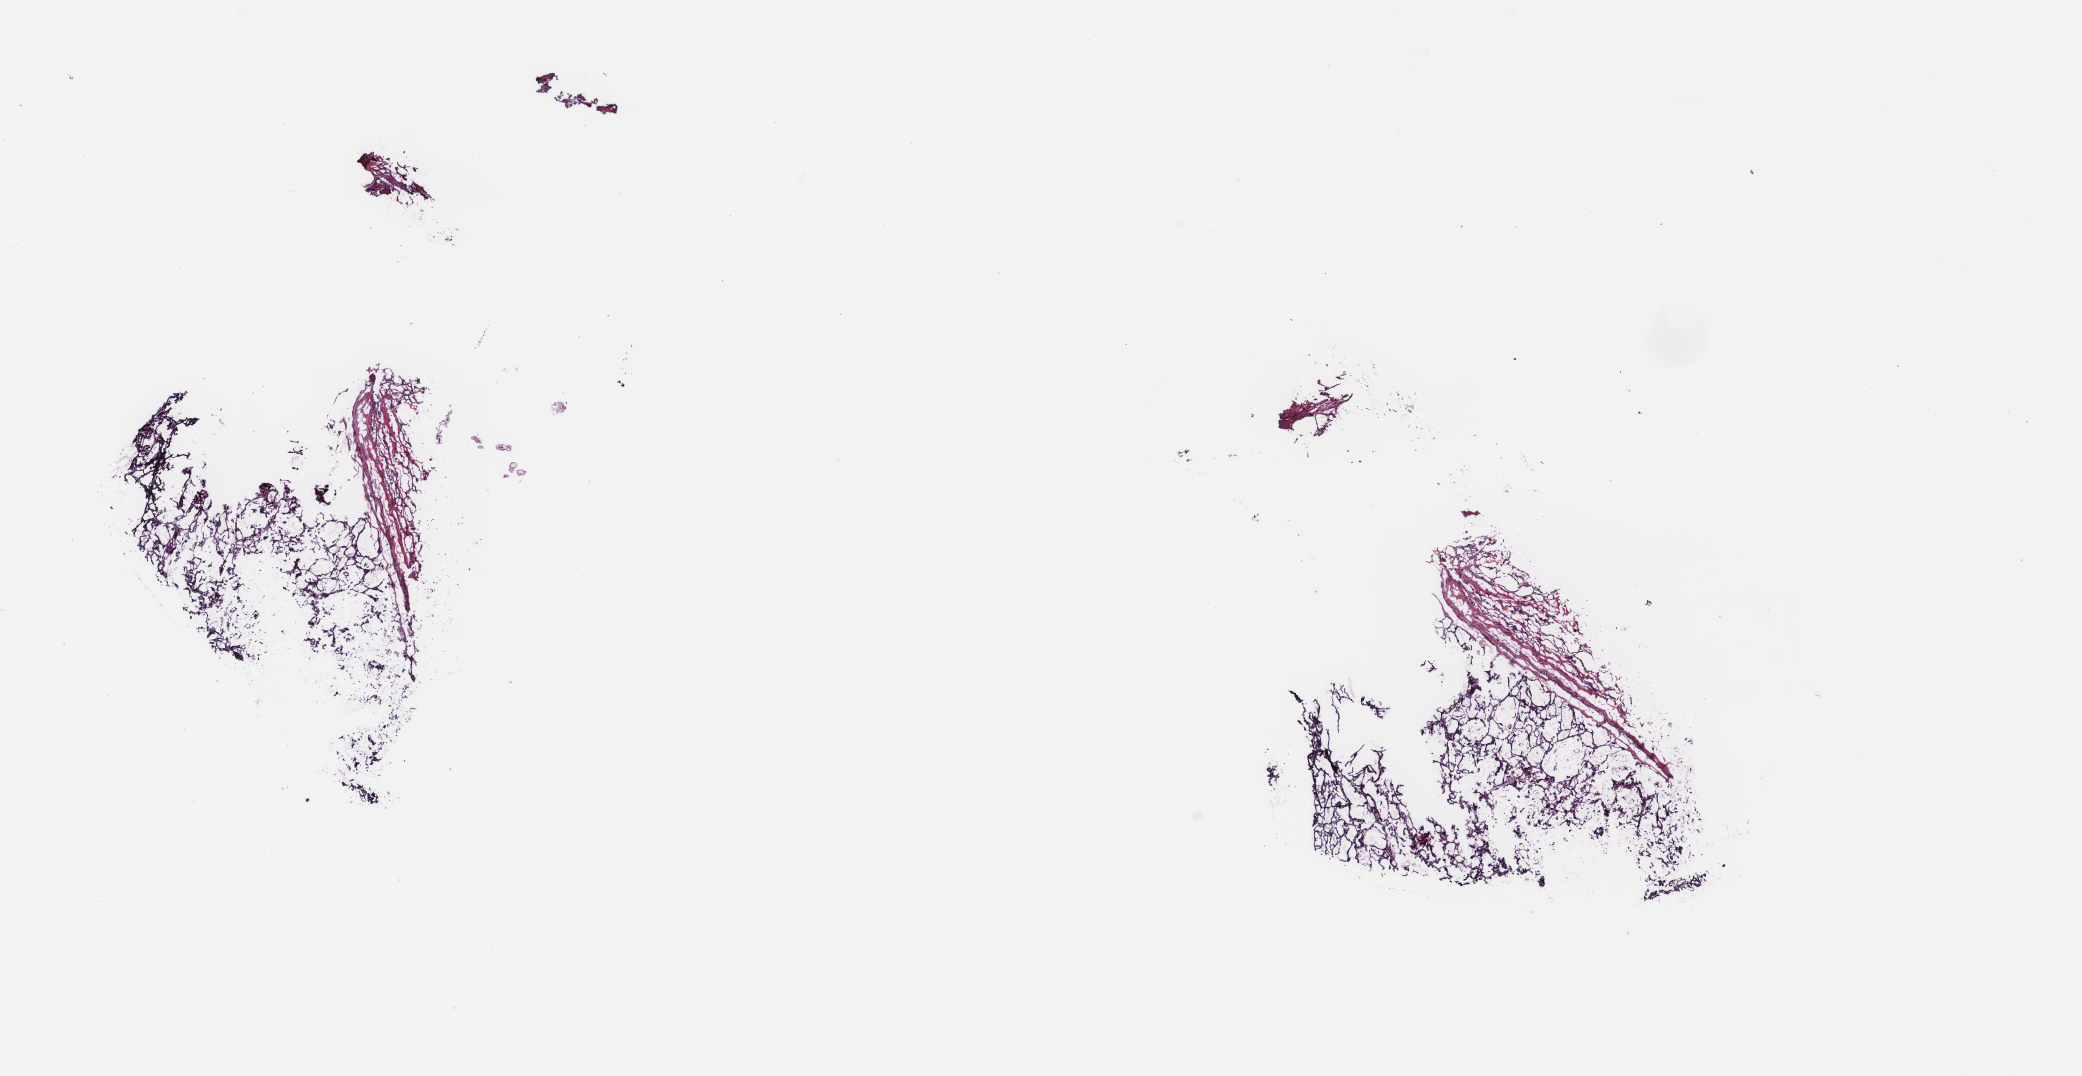
Whole-slide histology image, H&E — low-resolution overview of the scanned area, about 16.5 x 8.5 mm (acquisition: 40x scan). Frozen section from the top of the tissue portion. Sample: primary tumour, thyroid. Patient: female, age at initial diagnosis 44 years. Composition of this section per pathologist review: tumour cells 80%, tumour nuclei 80%, normal cells 10%, stromal cells 10%, necrosis 0%. Inflammatory infiltration, as recorded: lymphocyte infiltration 1%, monocyte infiltration 1%, neutrophil infiltration 0%.
* AJCC pathologic stage: I (7th edition)
* lymph nodes positive (case pathology): 15 of 30 examined
* pathologic diagnosis: Papillary adenocarcinoma, NOS